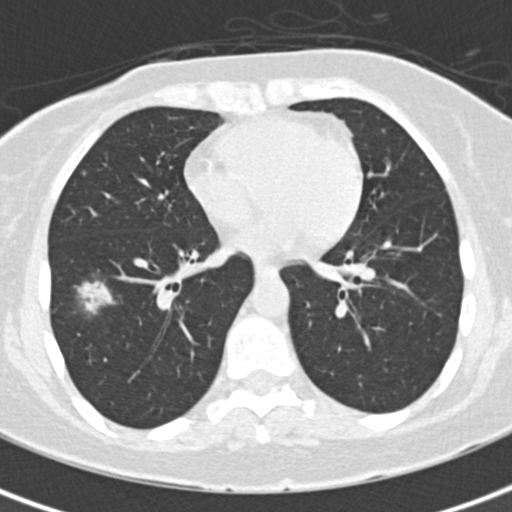
Axial slice from a low-dose chest CT screening exam, baseline annual screen, lung window (W 1500 / L -600 HU), 2 mm slice thickness, 120 kVp, slice 98 of 171 in the series, 512 × 512 image matrix, field of view 284 × 284 mm. Female participant, aged 56 years at enrolment. Former smoker at enrolment.
Expert reader's lesion annotation, bounding box [x1, y1, x2, y2] px = [66, 271, 129, 327]. The screening reader recorded 5 non-calcified nodules or masses ≥4 mm on this exam; which of them this box marks is not recorded. Official screen result: positive, change unspecified: nodule(s) >= 4 mm or enlarging nodule(s), mass(es), or other non-specific abnormalities suspicious for lung cancer. Participant outcome: lung cancer diagnosed 26 days after this screen — bronchiolo-alveolar carcinoma, mucinous, right lower lobe, well differentiated (G1), stage IA (AJCC 6th edition), 19 mm at pathology.